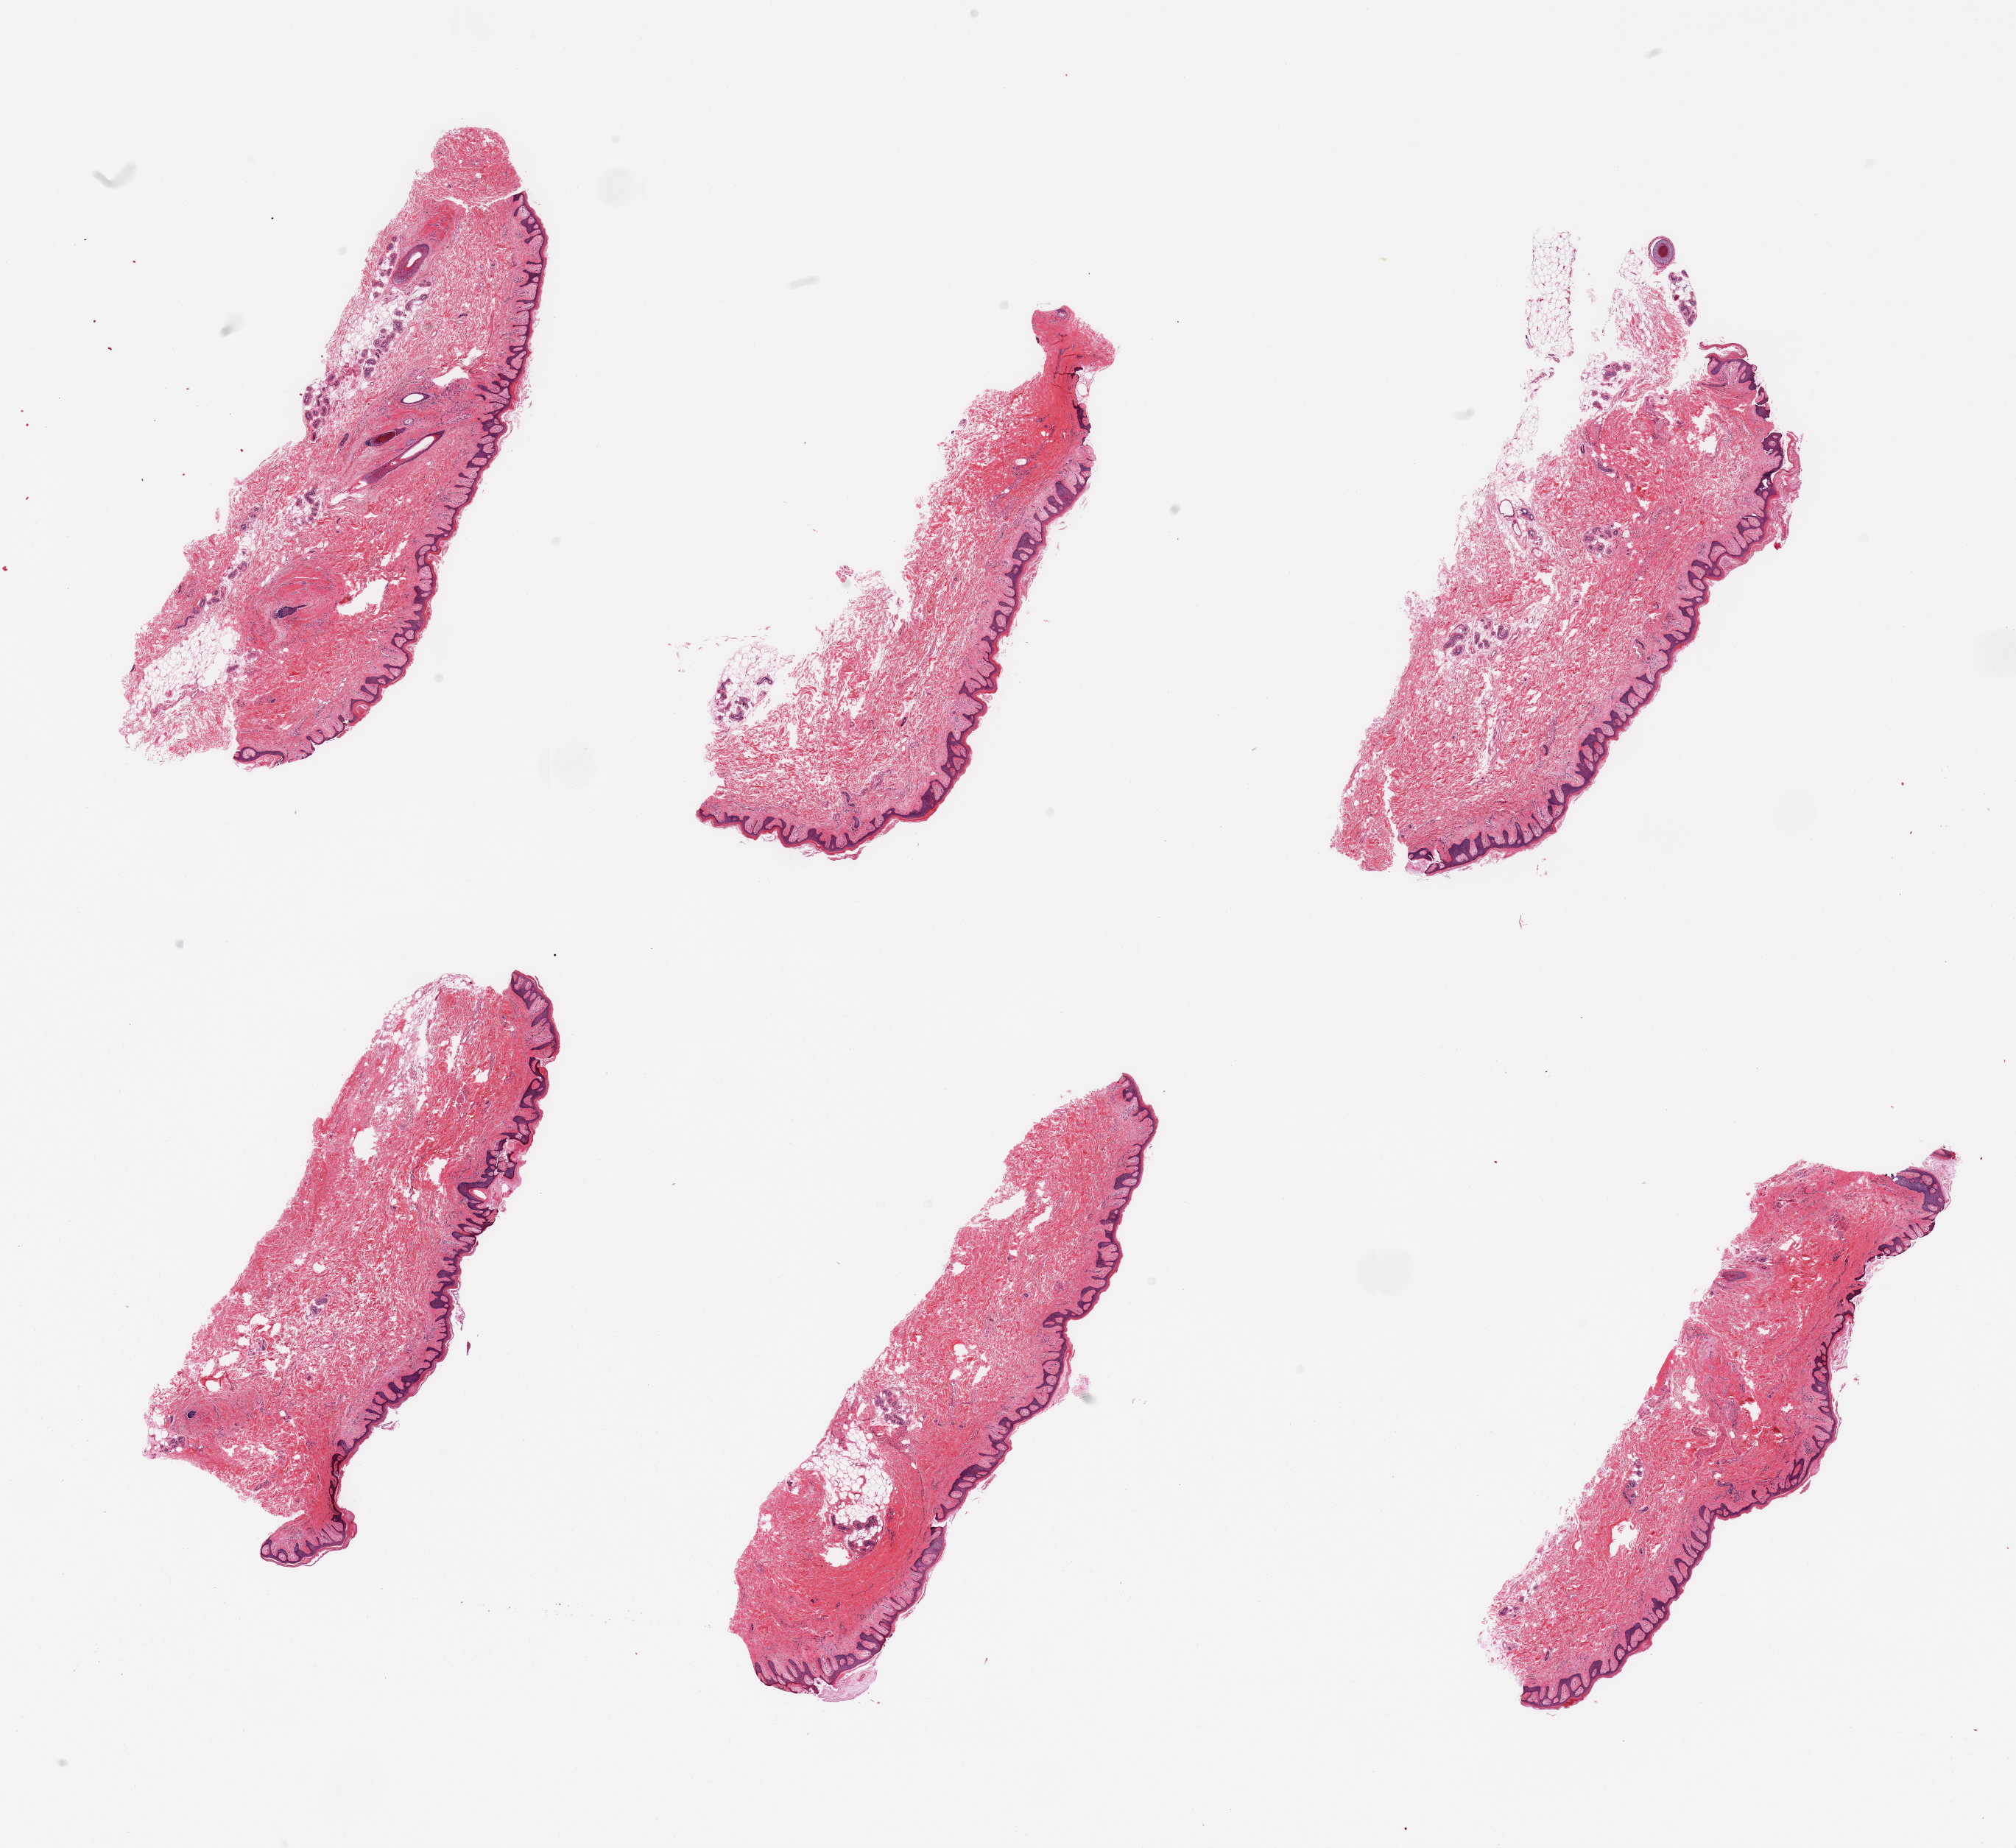
Digitized hematoxylin and eosin (H&E)-stained section, low-resolution overview of the scanned area, about 21.7 x 19.9 mm. PAXgene-fixed paraffin-embedded (PFPE) section. Section of skin of suprapubic region (target tissue). Tissue donor sample. Donor sex: female.
Review note (as recorded): 6 pieces; hyperkeratotic.